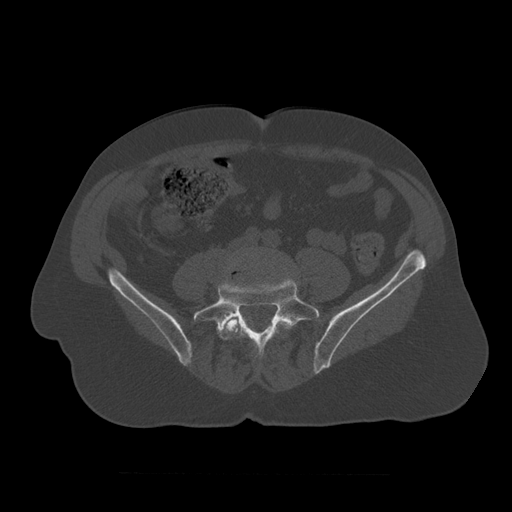
CT including the spine, one axial slice. Position 261 of 450 along the scan axis. 120 kVp. Bone window (W 1800 / L 400 HU). 512 × 512 image matrix, field of view 405 × 405 mm. Patient age 75 years. From the clinical record (not read from this slice): primary cancer: prostate.
Annotated regions visible in this slice (semi-automatic segmentation, software-assisted and operator-edited):
- L4 vertebra: bounding box <223,252,293,353> (left, top, right, bottom; pixels)
- L5 vertebra: <194,275,320,359>